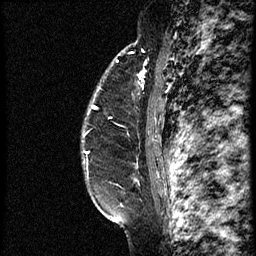
Breast MRI (dynamic contrast-enhanced), one sagittal slice; position 47 of 60 along the scan axis; dynamic contrast-enhanced study with each time point stored as its own series, time point 2 of 3 at this slice position (early post-contrast, ordered by acquisition time); 1.5 T; TE 4.2 ms, TR 18.9 ms; 2 mm slice thickness; 256 × 256 image matrix, field of view 200 × 200 mm. Female patient. From the clinical record (not read from this slice): setting: breast cancer imaged before/during neoadjuvant chemotherapy; receptor status: HER2-positive.
Structures marked on this image (semi-automatically segmented with operator editing):
- analysis volume of interest (the breast-tissue region the enhancement analysis was run in; not a lesion): bounding box [x1, y1, x2, y2] px = [82, 66, 161, 147]
- tumour enhancement mask (voxels above the 100 % enhancement threshold inside the analysis volume of interest): [88, 75, 141, 116]